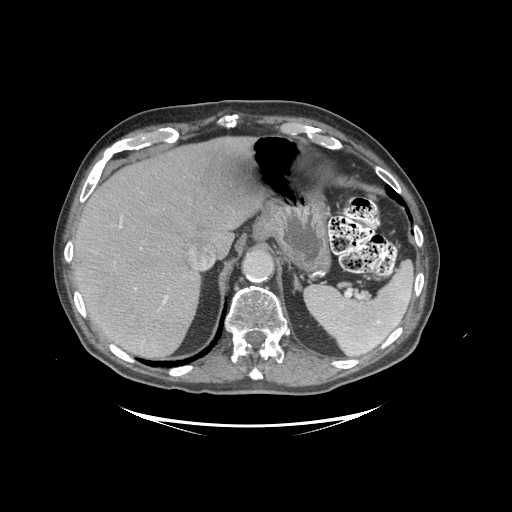
Contrast-enhanced abdominal CT (liver protocol), one axial slice; slice 74 of 99 in the series (ordered by position); 140 kVp; soft-tissue window (W 400 / L 40 HU); 2.5 mm slice thickness; 512 × 512 image matrix, field of view 460 × 460 mm. Case-level facts recorded for this patient, not image findings: diagnosis: hepatocellular carcinoma (patient treated with transarterial chemoembolisation; whether this scan precedes or follows treatment is not stated here); TNM stage (as recorded): Stage-I; Child-Pugh class: A; tumour differentiation: moderately differentiated; tumour nodularity: uninodular.
Structures marked on this image (semi-automatically segmented with operator editing):
- liver parenchyma outside the tumour (the mass and vessels are separate outlines, so this box may not span the whole liver): box from (x=72, y=136) to (x=264, y=356) px
- liver vessels: (x=119, y=224)–(x=205, y=305)